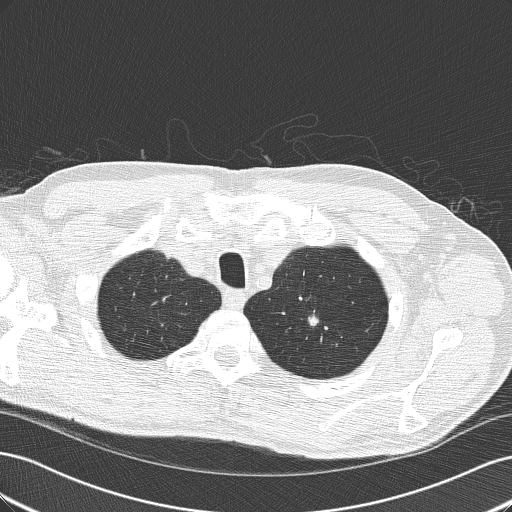
Low-dose screening chest CT, one axial slice; position 158 of 189 along the scan axis; reconstruction kernel B50f; 120 kVp; lung window (W 1500 / L -600 HU); 512 × 512 image matrix.
Structures marked on this image (expert manual segmentation):
- lesion 1 (tumor, upper lobe of left lung): bounding box [x1, y1, x2, y2] px = [308, 310, 319, 328]